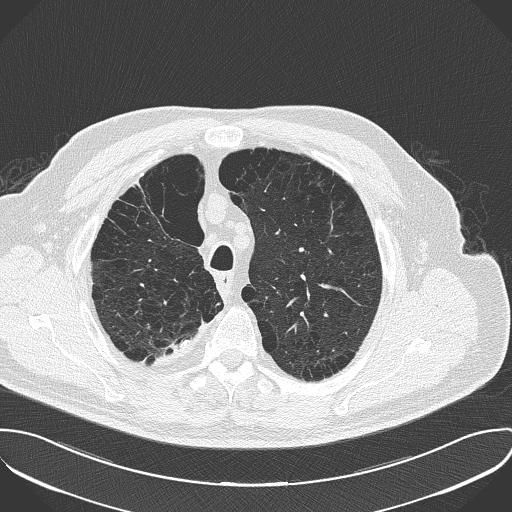
Axial slice from a low-dose chest CT screening exam. Baseline screening round. Lung window (W 1500 / L -600 HU). 2 mm slice thickness. Slice 40 of 181 in the series. 512 × 512 image matrix, field of view 388 × 388 mm. Male participant, aged 68 years at enrolment. Current smoker at enrolment.
- Expert reader's lesion annotation, box from (x=126, y=324) to (x=197, y=375) px.
- The screening reader recorded 3 non-calcified nodules or masses ≥4 mm on this exam (left lower lobe, left upper lobe, right lower lobe); which of them this box marks is not recorded.
- Later outcome: lung cancer diagnosed 661 days after this screen — adenocarcinoma, NOS, right upper lobe, stage IV (AJCC 6th edition), 29 mm at pathology.